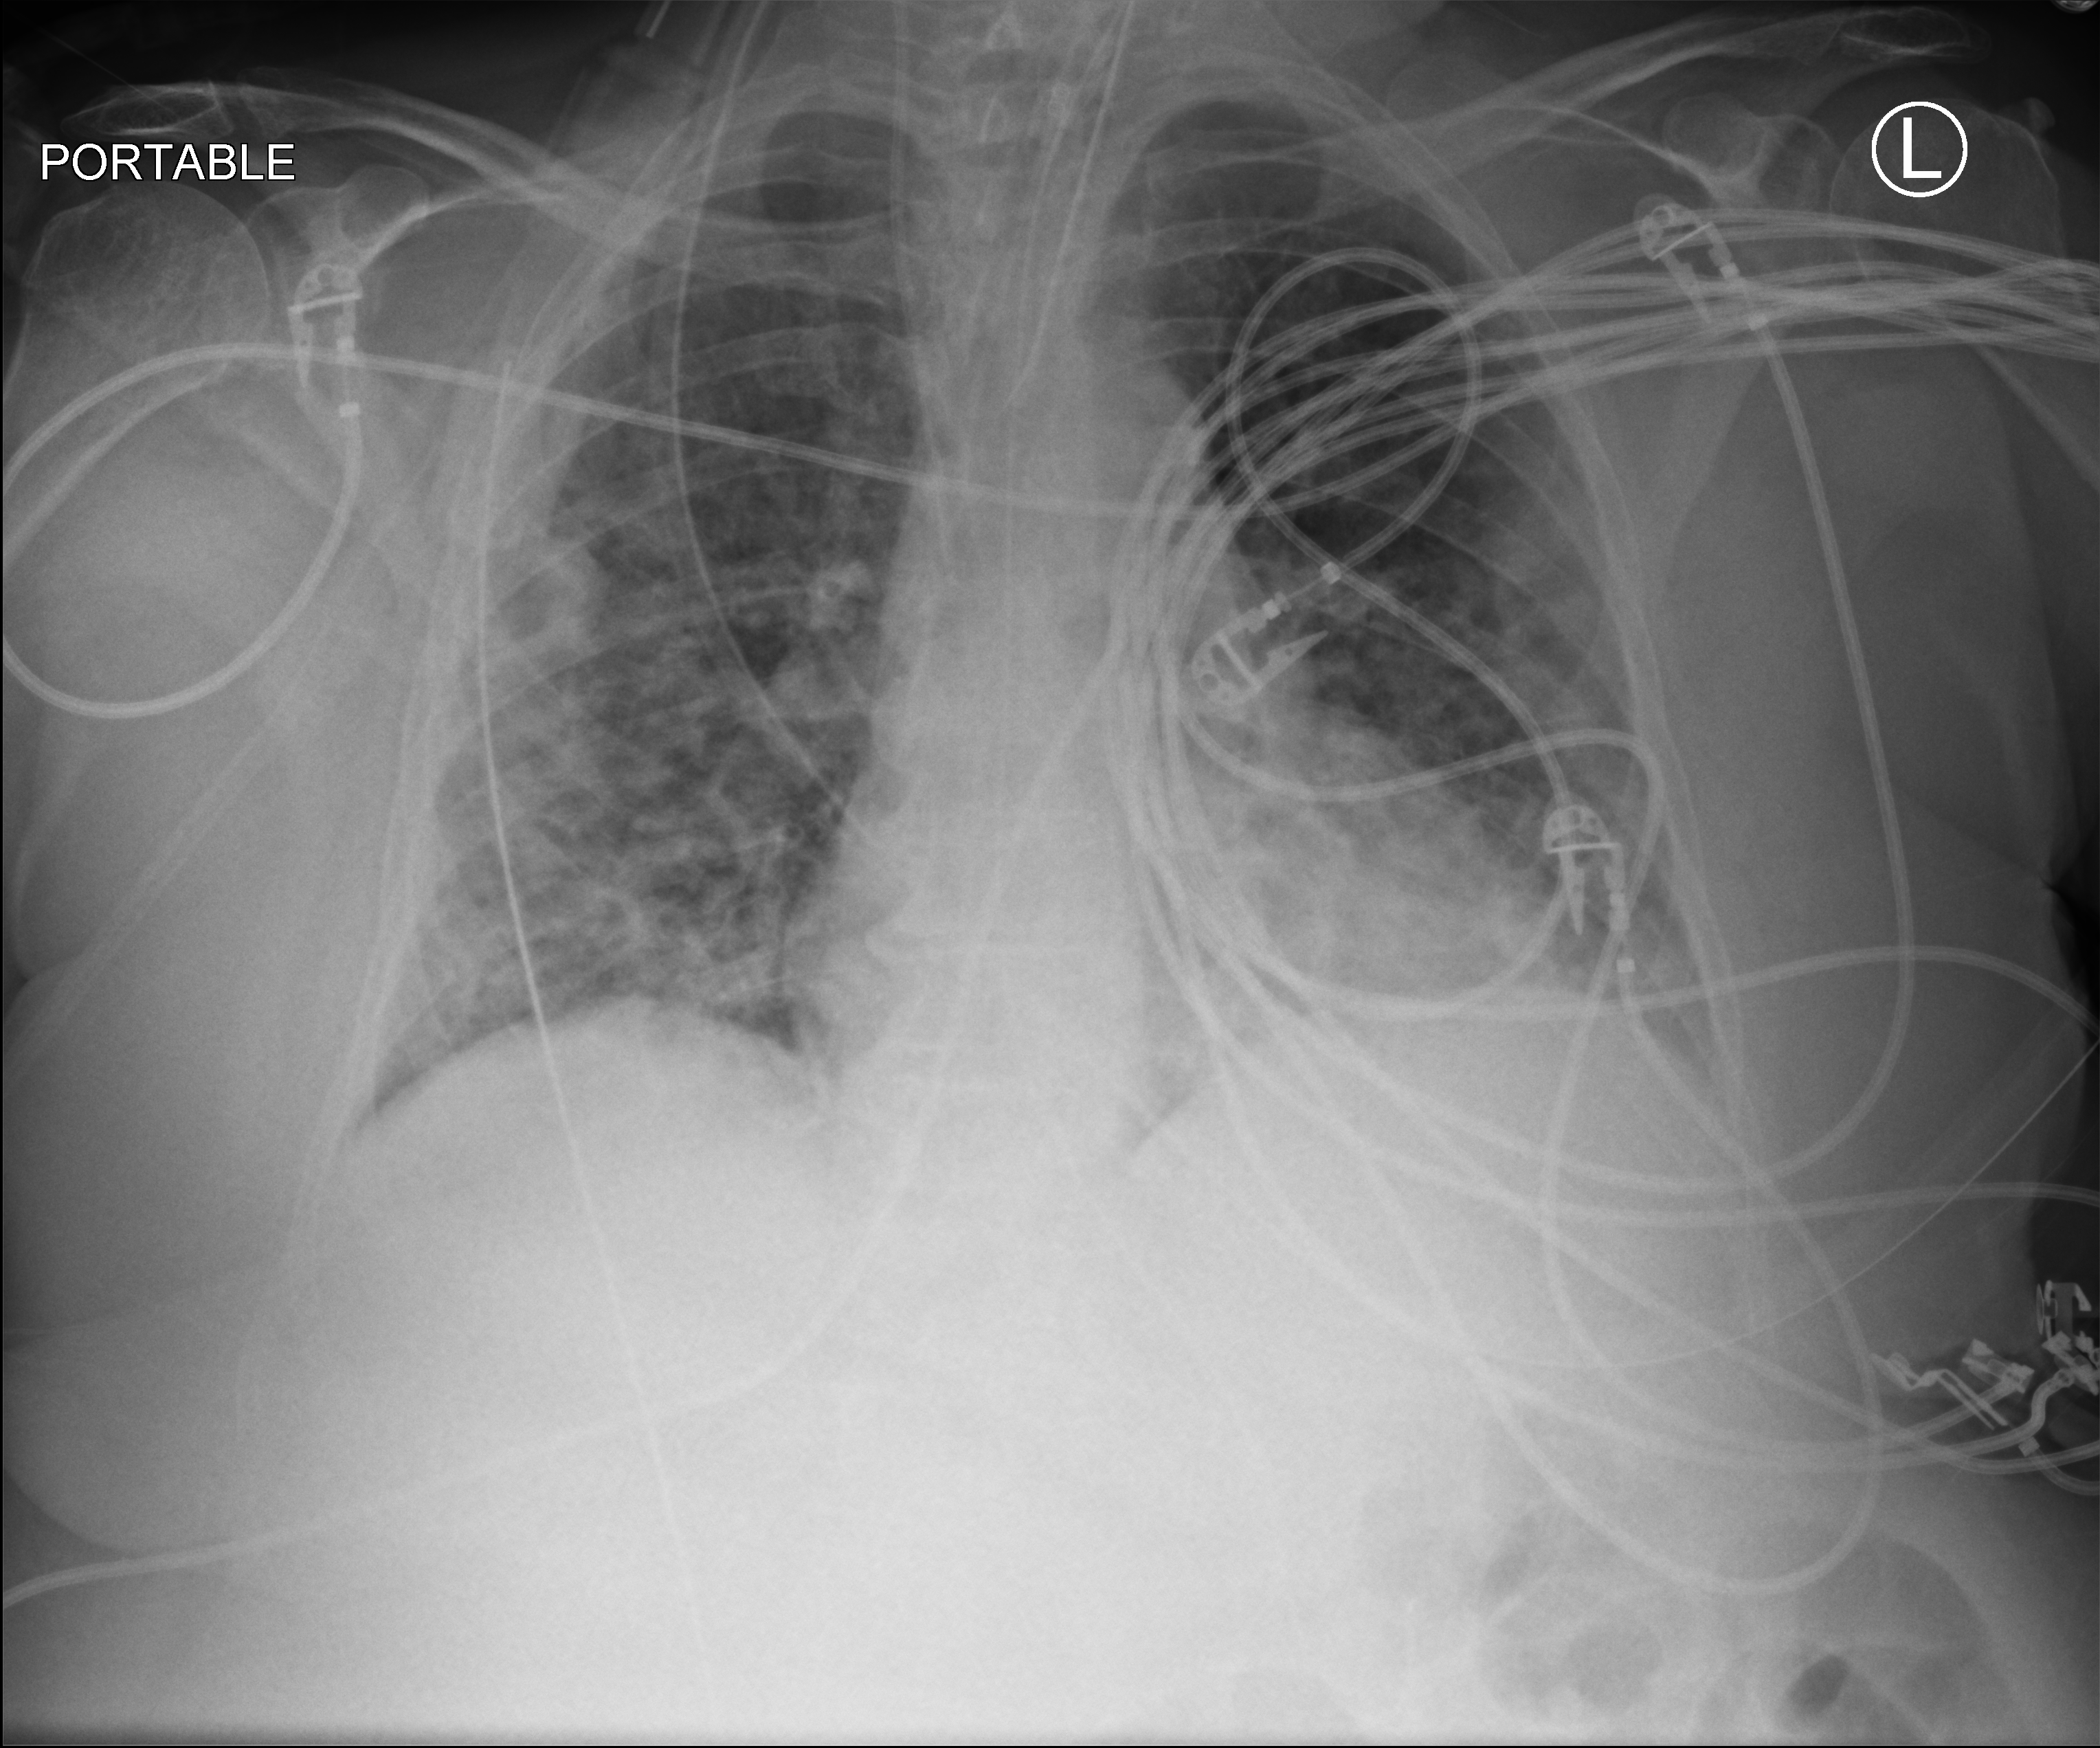
Chest X-ray (portable). Patient hospitalised with COVID-19; female, aged 75–90 years.
Hospital-stay facts (about this admission, not read from this image; timing relative to this image not recorded): mechanically ventilated during this hospital stay: yes; admitted to intensive care during this hospital stay: yes.